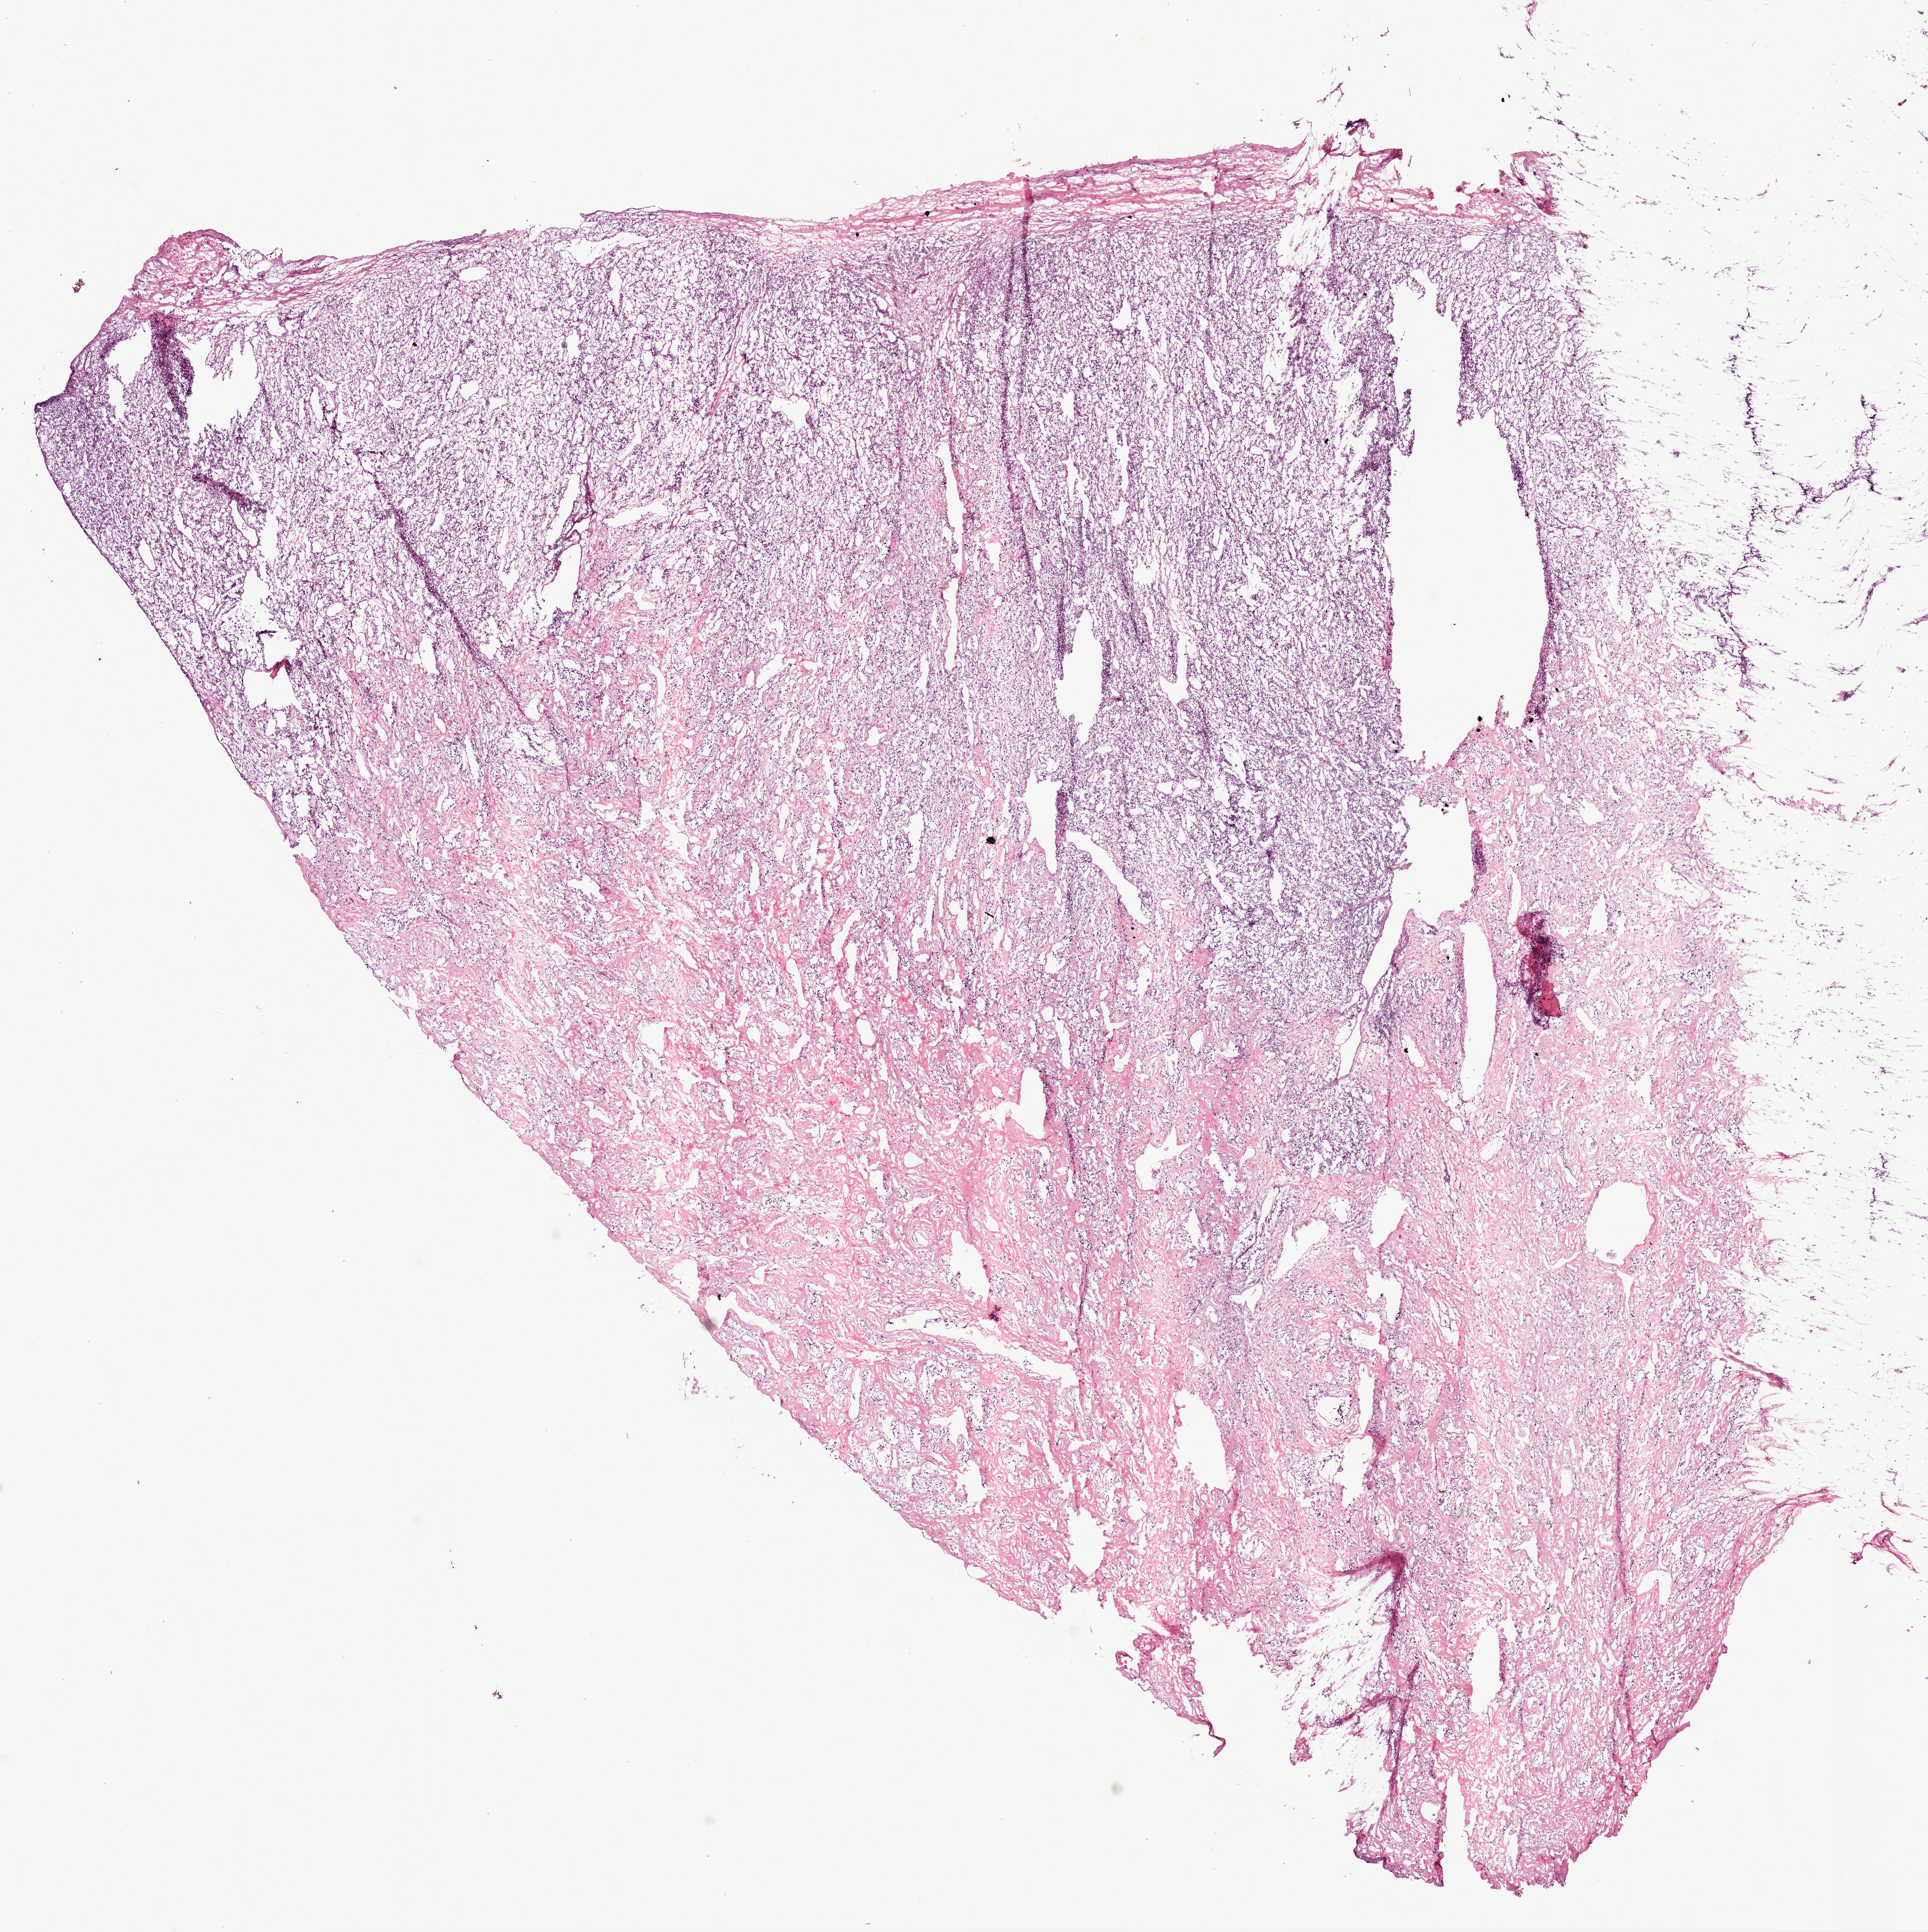
Digitized Hematoxylin and eosin (H&E) stained tissue section (whole slide) — whole scanned area (about 12.0 x 12.1 mm, acquisition: 20x scan) shown as a low-resolution overview; frozen section from the bottom of the tissue portion; sample: primary tumour, kidney. Patient: male, age at initial diagnosis 69 years. Histologic grade: G2 (moderately differentiated). Composition of this section per pathologist review: tumour cells 65%, tumour nuclei 80%, normal cells 0%, stromal cells 35%, necrosis 0%.
Pathologic diagnosis: Clear cell adenocarcinoma, NOS. Laterality: left. AJCC pathologic stage: IV (6th edition).